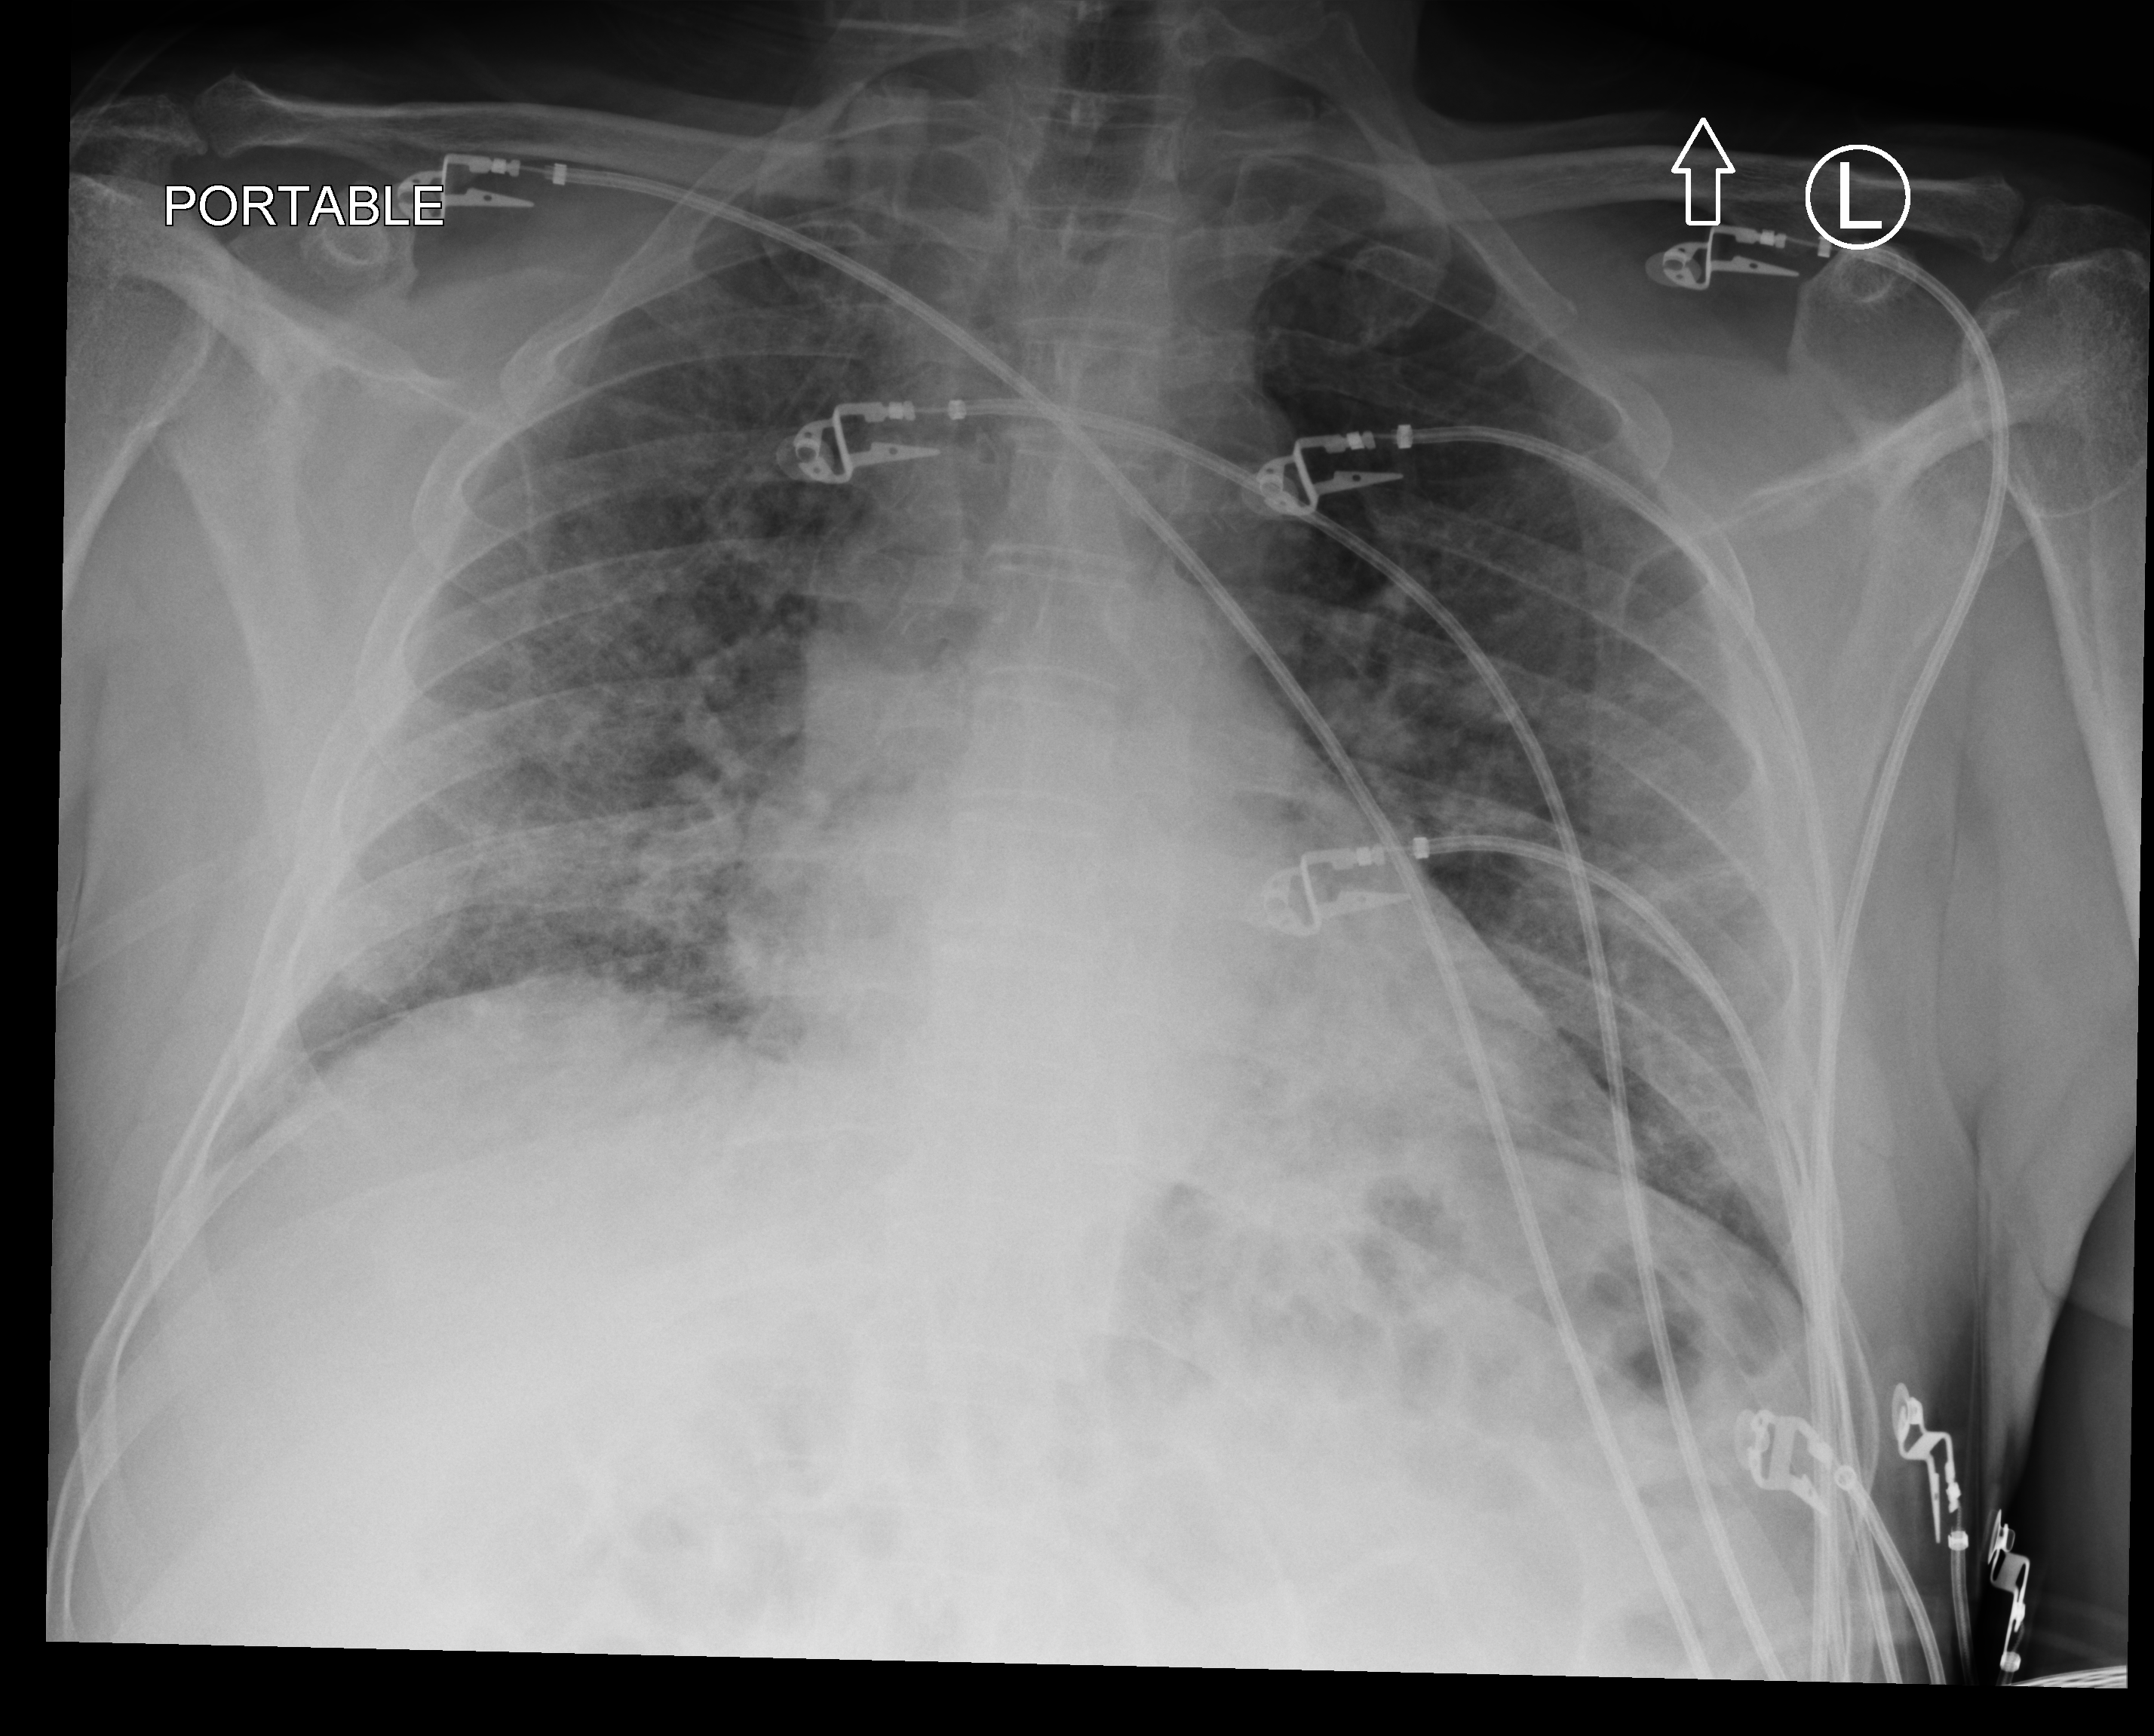
Bedside chest radiograph (computed radiography); anteroposterior (AP) projection. Patient hospitalised with COVID-19; male, aged 60–74 years.
Admission-level facts for this patient (not findings on this image; timing relative to this image not recorded):
- diabetes (admission record): yes